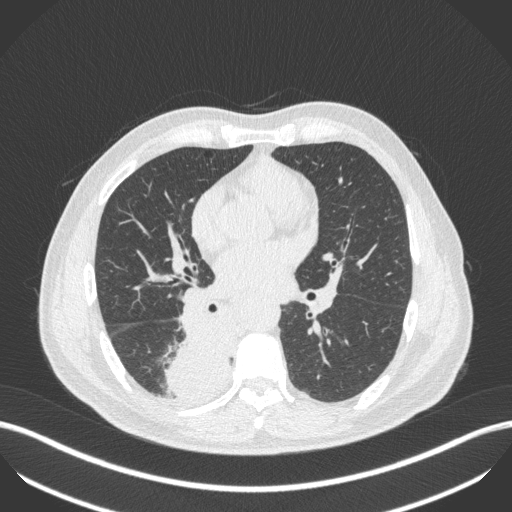
Chest CT, one axial slice. Slice 237 of 451 in the series (ordered by position). Reconstruction kernel B31f. 100 kVp. Lung window (W 1500 / L -600 HU). 1 mm slice thickness. 512 × 512 image matrix, field of view 400 × 400 mm. Patient: male, 61 years. Case-level facts recorded for this patient, not image findings: clinical TNM (as recorded): T1 N0 M0.
Structures marked on this image (bounding box drawn by a radiologist):
- lung tumour (recorded histology: small cell carcinoma): box from (x=155, y=303) to (x=236, y=394) px